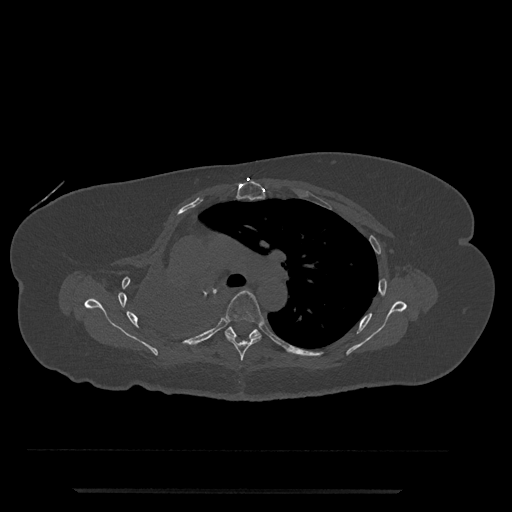
CT including the spine, one axial slice. Reconstruction kernel Br40s/3. 120 kVp. Bone window (W 1800 / L 400 HU). 0.5 mm slice thickness. 512 × 512 image matrix, field of view 440 × 440 mm. Patient: female, 51 years. Case-level facts recorded for this patient, not image findings: primary cancer: neuro.
Annotated regions visible in this slice (semi-automatic segmentation, software-assisted and operator-edited):
- T5 vertebra: bounding box <223,290,265,361> (left, top, right, bottom; pixels)
- T6 vertebra: <225,326,261,339>